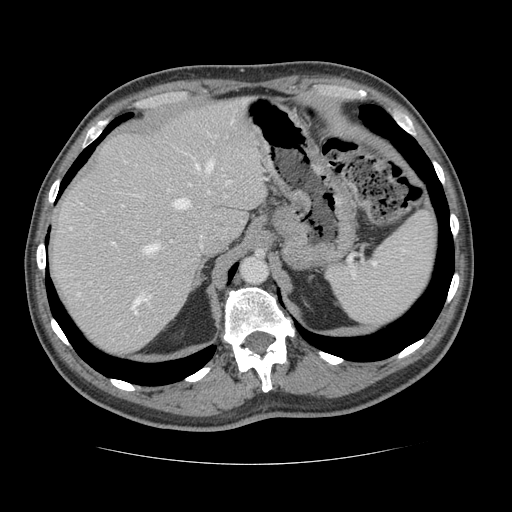
Contrast-enhanced abdominal CT, one axial slice. Position 97 of 134 along the scan axis. 120 kVp. Intravenous contrast given. Soft-tissue window (W 400 / L 40 HU). 2.5 mm slice thickness. 512 × 512 image matrix, field of view 377 × 377 mm. Male patient, age 68 years. Case-level facts recorded for this patient, not image findings: diagnosis: colorectal cancer liver metastases, imaged before liver resection.
Outlined on this slice (manually delineated by an expert):
- hepatic veins: box from (x=77, y=161) to (x=213, y=313) px
- liver: (x=51, y=101)–(x=266, y=355)
- planned liver remnant (the part of the liver to remain after resection): (x=51, y=100)–(x=267, y=329)
- portal vein (with intrahepatic branches): (x=112, y=181)–(x=230, y=297)